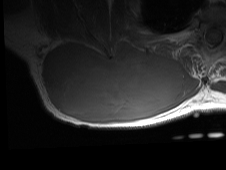
MRI of an extremity soft-tissue mass, one axial slice. Position 39 of 81 along the scan axis. MR volume resampled by the dataset authors to the PET/CT grid (not the native acquisition matrix). 3.27 mm slice thickness. 226 × 170 image matrix, field of view 221 × 166 mm. Male patient. Case-level facts recorded for this patient, not image findings: histological type: pleiomorphic spindle cell undifferentiated; grade: high; site of the primary tumour: right parascapusular.
Structures marked on this image (expert contour drawn on MRI and transferred to this co-registered scan by the dataset authors):
- gross tumour volume including surrounding oedema: box from (x=41, y=40) to (x=200, y=125) px
- gross tumour volume (mass): (x=41, y=42)–(x=184, y=123)